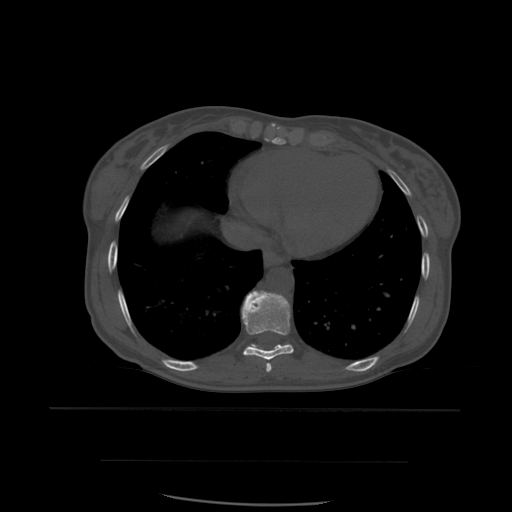
CT including the spine, one axial slice; slice 334 of 574 in the series (ordered by position); bone window (W 1800 / L 400 HU); 1.25 mm slice thickness; 512 × 512 image matrix. Patient age 48 years. From the clinical record (not read from this slice): primary cancer: lung.
Outlined on this slice (semi-automatic segmentation, software-assisted and operator-edited):
- T8 vertebra: bounding box (x1, y1, x2, y2) in pixels: (266, 363, 272, 373)
- T9 vertebra: (242, 291, 294, 361)